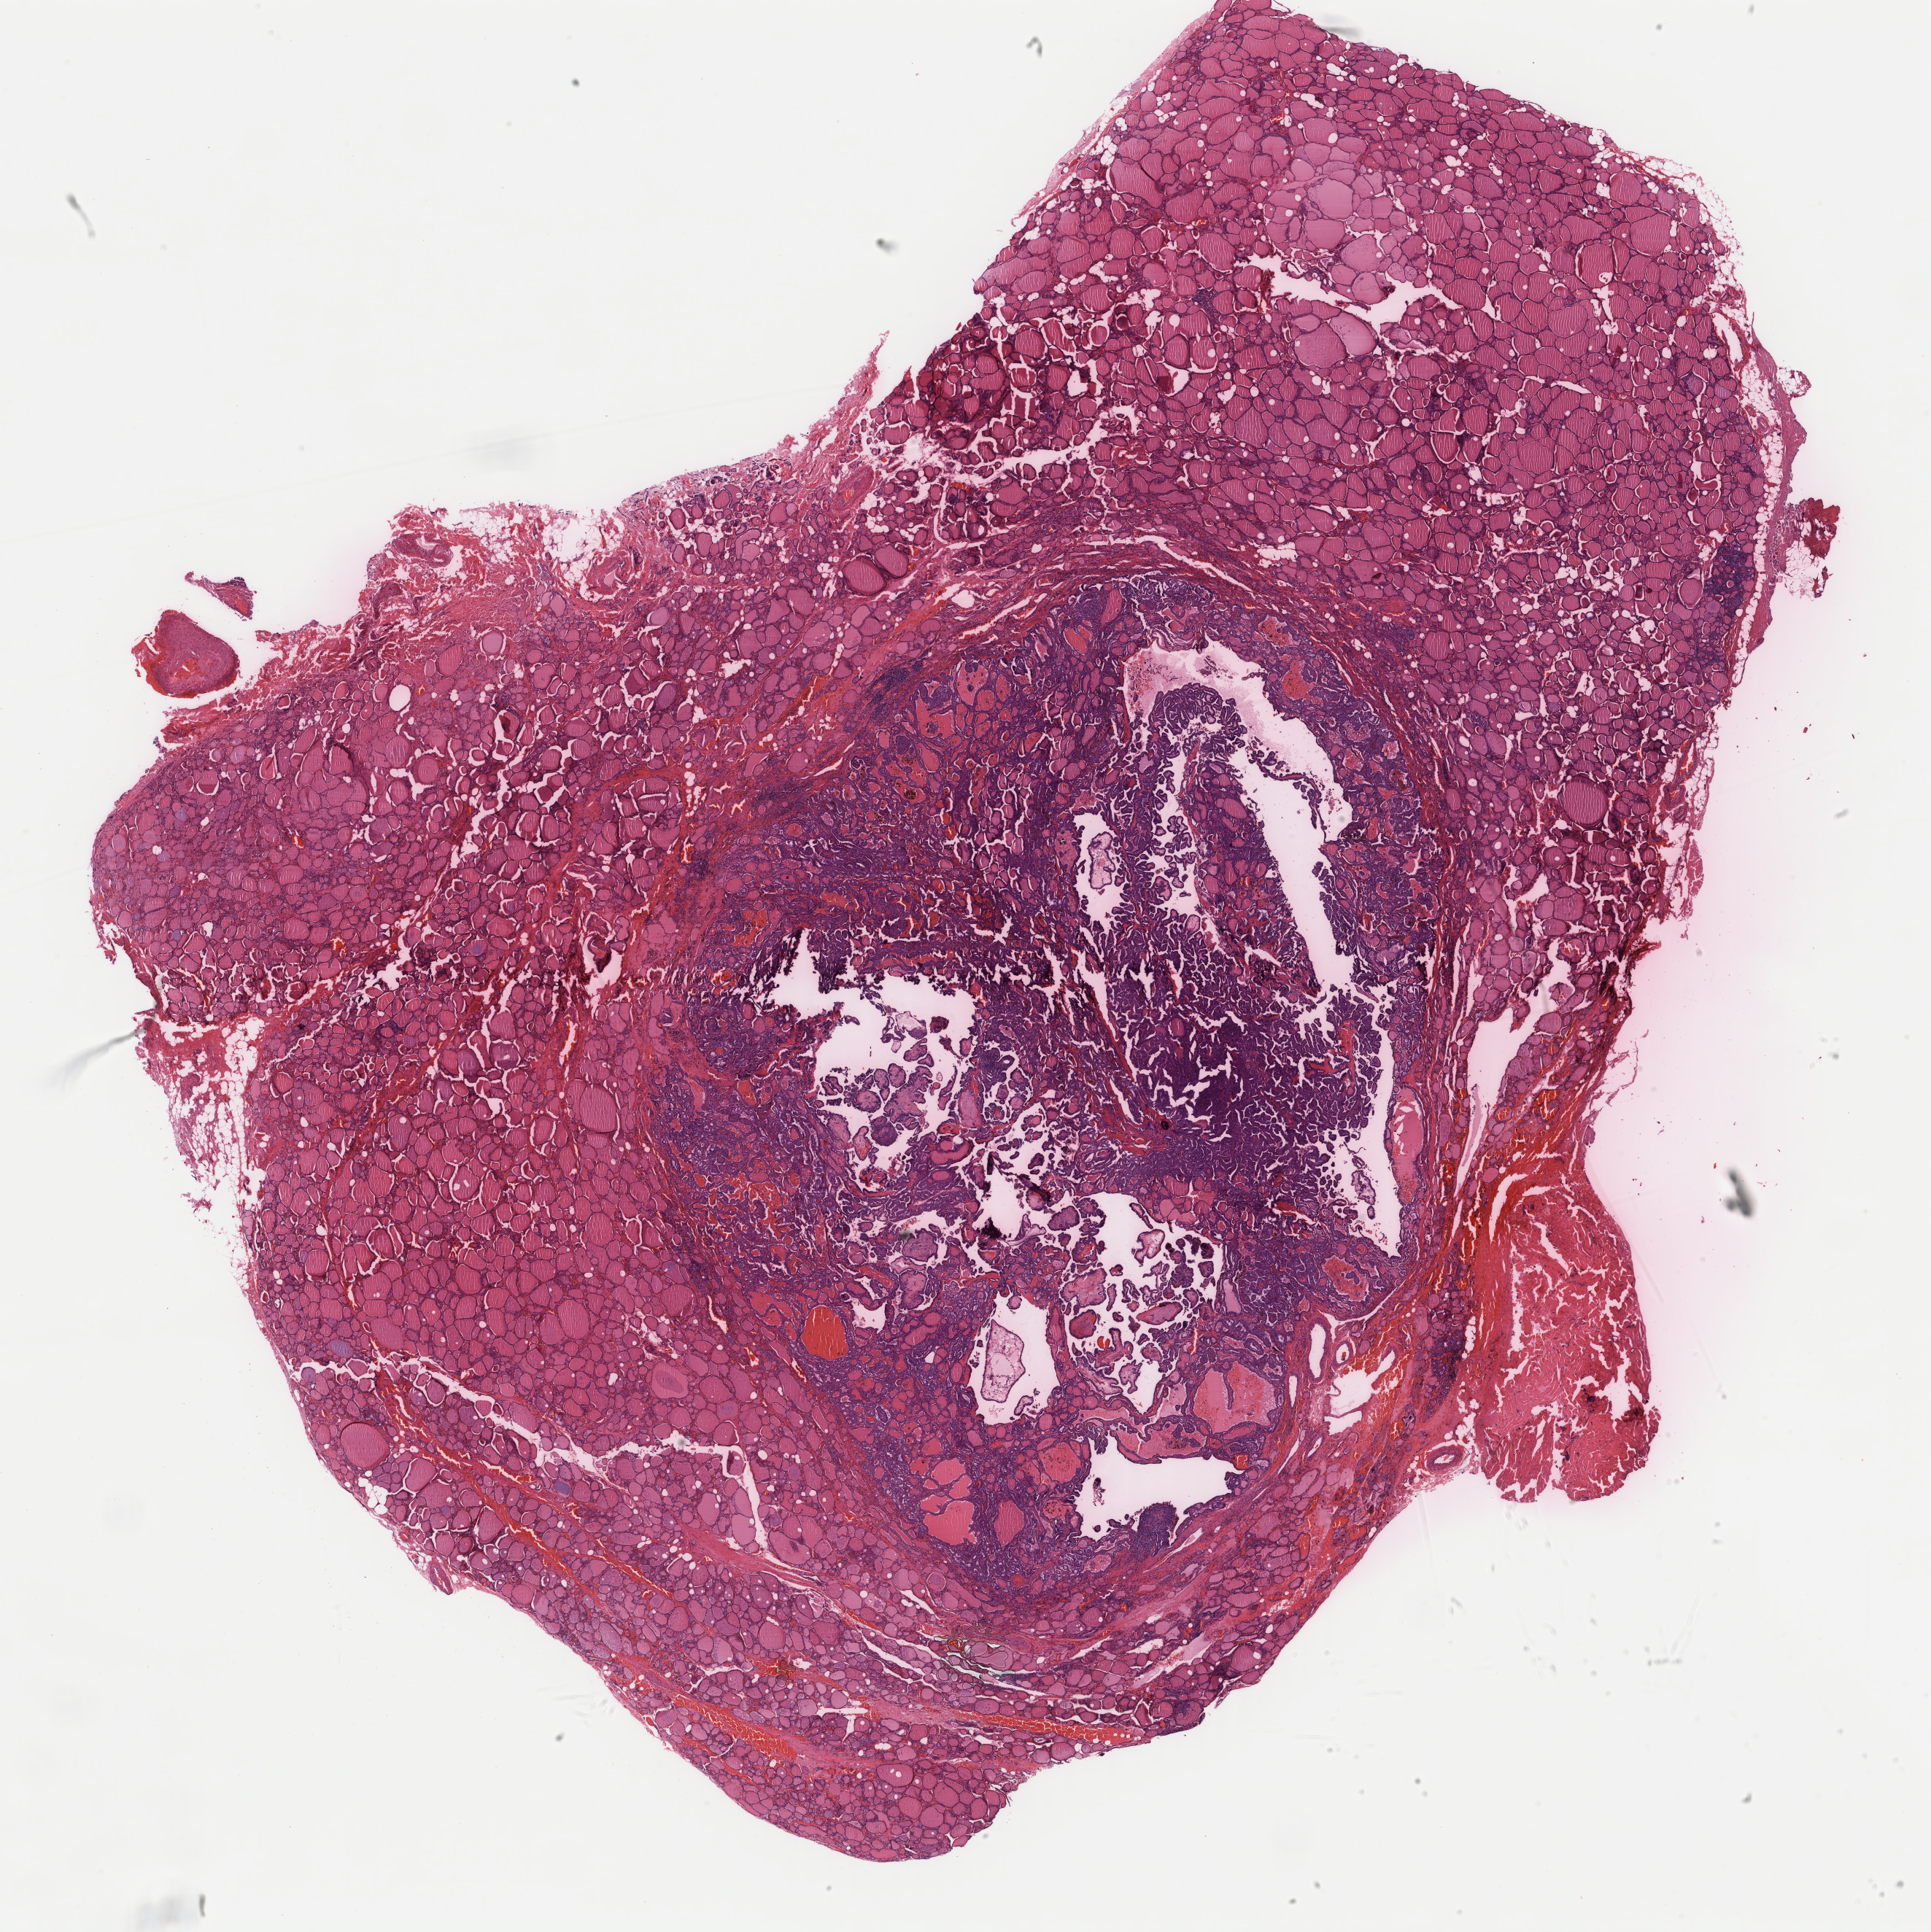
H&E whole-slide image — shown as a low-resolution overview of the whole scanned area (about 21.0 x 21.0 mm), formalin-fixed paraffin-embedded (FFPE) diagnostic section, thyroid, primary tumour sample. Female, age 65 years at initial diagnosis.
Diagnosis: Papillary adenocarcinoma, NOS. Lymph nodes positive (case pathology): 0 of 1 examined. AJCC pathologic stage: III (6th edition).